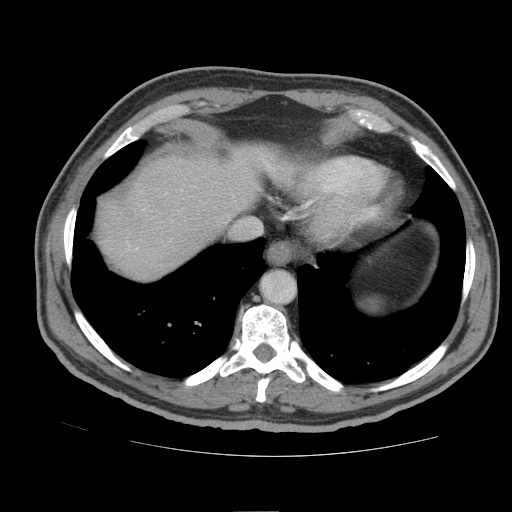
Contrast-enhanced abdominal CT (liver protocol), one axial slice. Position 77 of 105 along the scan axis. Soft-tissue window (W 400 / L 40 HU). 2.5 mm slice thickness. 512 × 512 image matrix, field of view 380 × 380 mm. Case-level facts recorded for this patient, not image findings: diagnosis: hepatocellular carcinoma (patient treated with transarterial chemoembolisation; whether this scan precedes or follows treatment is not stated here); TNM stage (as recorded): Stage-IIIB; Child-Pugh class: A; tumour nodularity: multinodular.
Annotated regions visible in this slice (semi-automatically segmented with operator editing):
- liver parenchyma outside the tumour (the mass and vessels are separate outlines, so this box may not span the whole liver): bounding box <98,146,284,280> (left, top, right, bottom; pixels)